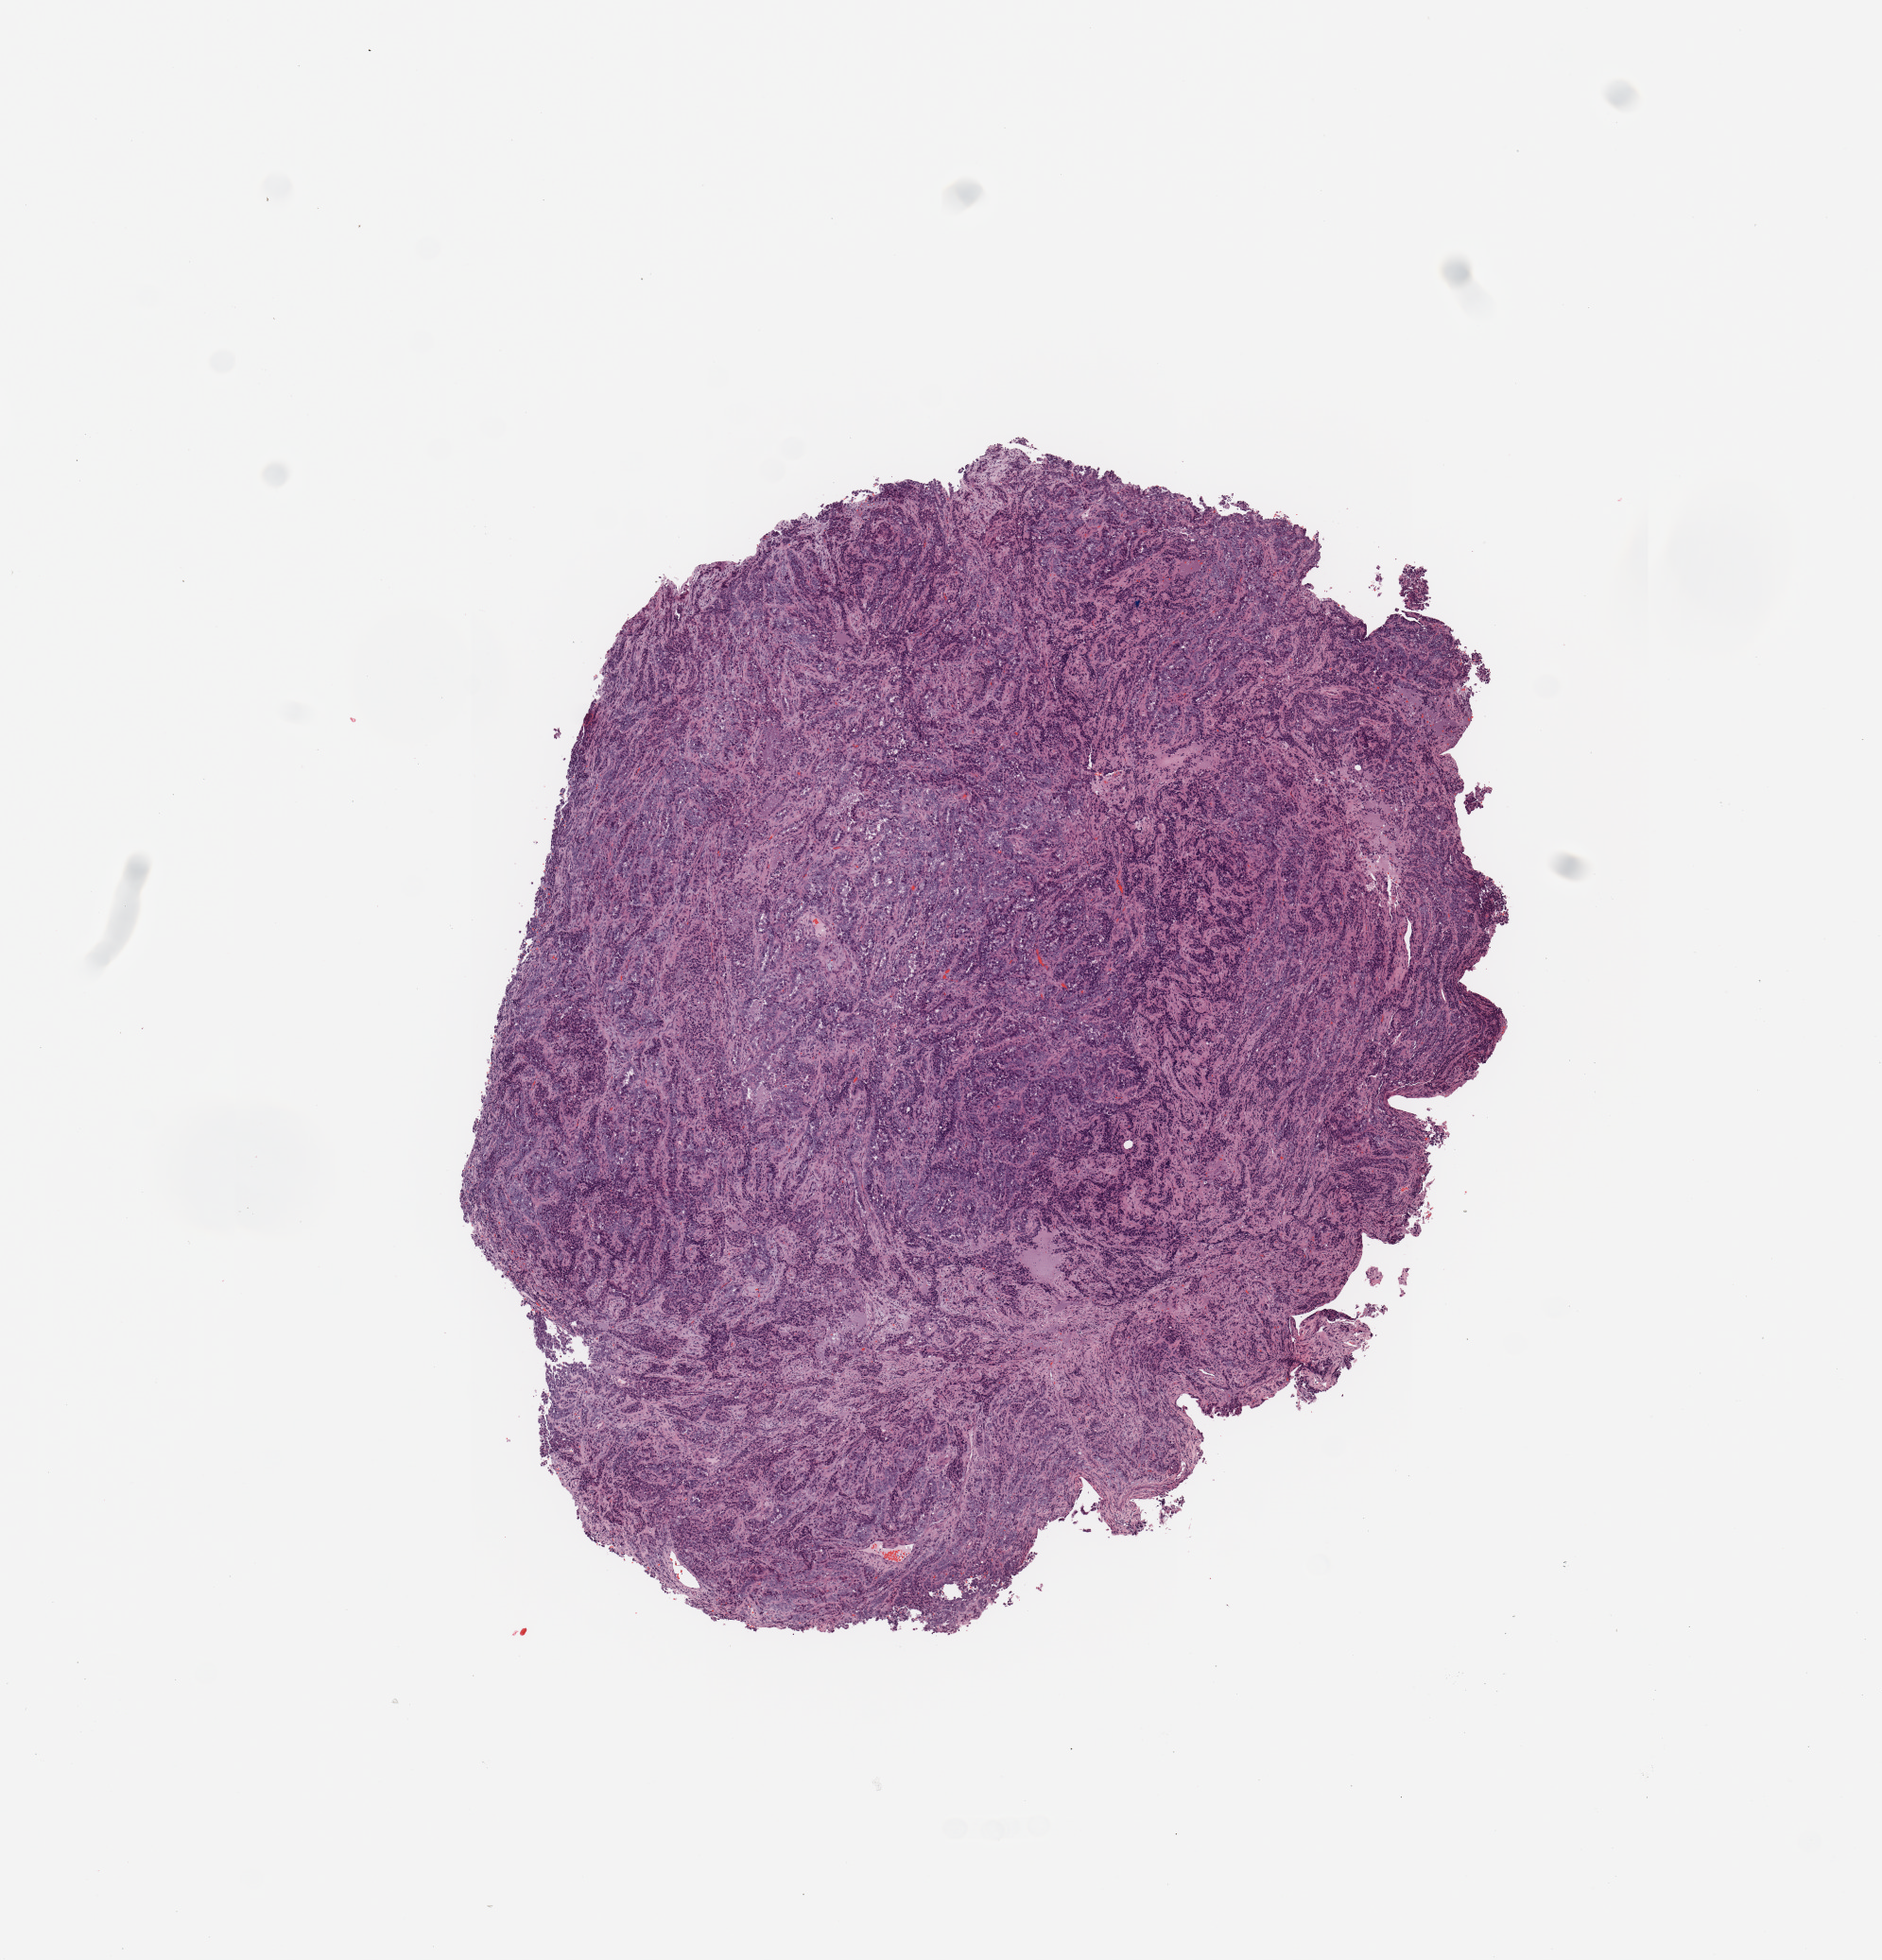
H&E whole-slide image, whole scanned area (about 7.9 x 8.2 mm, slide scanned at 20x) shown as a low-resolution overview; uterus, tumour tissue. 68-year-old female patient. Histologic grade: G3 (poorly differentiated).
- AJCC pathologic stage: III
- diagnosis: Endometrioid adenocarcinoma, NOS